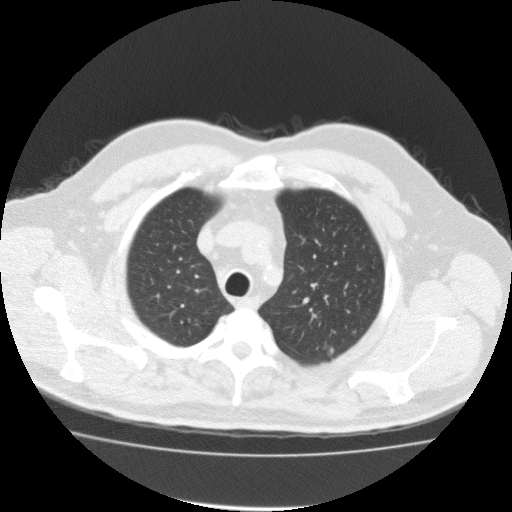
Chest CT (low-dose screening protocol), one axial image, baseline annual screen, lung window (W 1500 / L -600 HU), 2 mm slice thickness, standard (soft-tissue) reconstruction kernel (FC10), 120 kVp, 512 × 512 image matrix. Male, age 57 years at enrolment. Former smoker at enrolment.
- Lesion marked by an expert reader, bounding box (x1, y1, x2, y2) in pixels: (318, 336, 347, 367).
- Screening reader's record for this exam (one nodule recorded; not confirmed to be the boxed lesion): non-calcified nodule or mass ≥4 mm, left upper lobe, 11 × 8 mm, spiculated (stellate) margins, soft tissue attenuation.
- Lung cancer was diagnosed 19 days after this screen: bronchiolo-alveolar adenocarcinoma, NOS, left upper lobe, well differentiated (G1), stage IA (AJCC 6th edition), 80 mm at pathology.